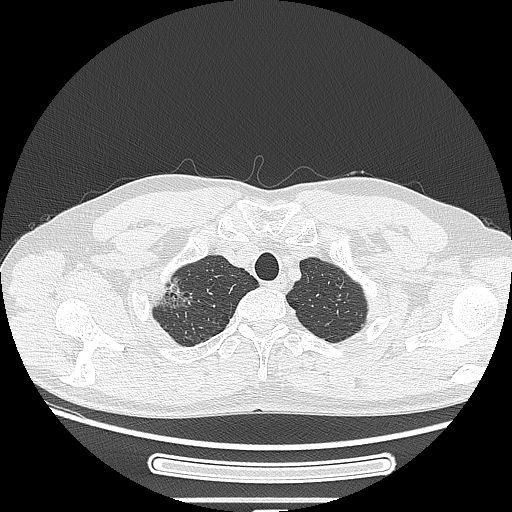
Chest CT, one axial slice; slice 235 of 269 in the series (ordered by position); 120 kVp; lung window (W 1500 / L -600 HU); 1.25 mm slice thickness; 512 × 512 image matrix, field of view 382 × 382 mm. Patient: male, 53 years. Case-level facts recorded for this patient, not image findings: clinical TNM (as recorded): T1c N0 M0; histopathological grade: G2.
Outlined on this slice (bounding box drawn by a radiologist):
- lung tumour (recorded histology: adenocarcinoma): box from (x=135, y=271) to (x=198, y=318) px